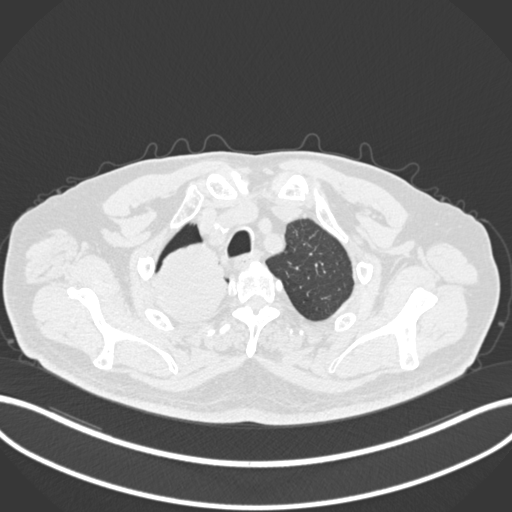
Chest CT, one axial slice; position 185 of 218 along the scan axis; reconstruction kernel B30f; lung window (W 1500 / L -600 HU); 512 × 512 image matrix. Male patient, age 68 years. From the clinical record (not read from this slice): clinical TNM (as recorded): T2a N0 M0.
Annotated regions visible in this slice (bounding box drawn by a radiologist):
- lung tumour (recorded histology: adenocarcinoma): bounding box [x1, y1, x2, y2] px = [148, 244, 228, 324]